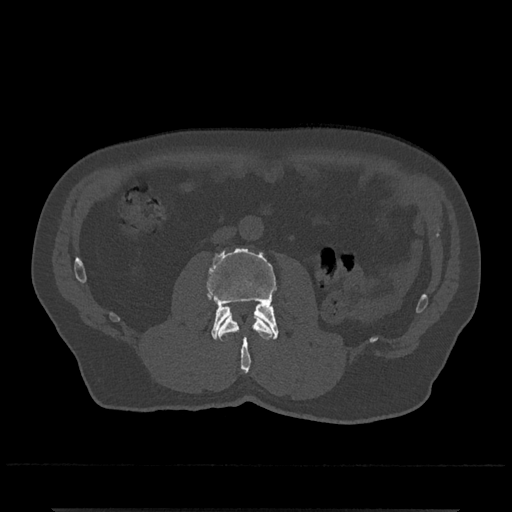
CT including the spine, one axial slice; slice 249 of 797 in the series (ordered by position); bone window (W 1800 / L 400 HU); 0.5 mm slice thickness; 512 × 512 image matrix, field of view 393 × 393 mm. Male patient, age 67 years. From the clinical record (not read from this slice): primary cancer: prostate.
Annotated regions visible in this slice (semi-automatic segmentation, software-assisted and operator-edited):
- L2 vertebra: box from (x=217, y=314) to (x=273, y=373) px
- L3 vertebra: (x=206, y=247)–(x=278, y=341)